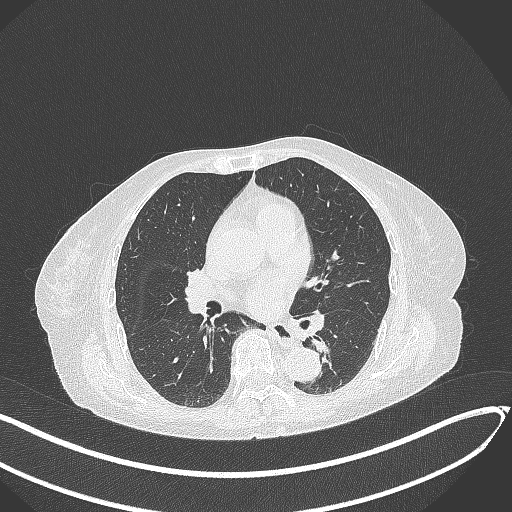
Chest CT, one axial slice; position 132 of 324 along the scan axis; reconstruction kernel B70f; lung window (W 1500 / L -600 HU); 512 × 512 image matrix, field of view 400 × 400 mm. Female patient, age 82 years. From the clinical record (not read from this slice): clinical TNM (as recorded): T1b N0 M1.
Structures marked on this image (bounding box drawn by a radiologist):
- lung tumour (recorded histology: adenocarcinoma): box from (x=311, y=333) to (x=332, y=356) px